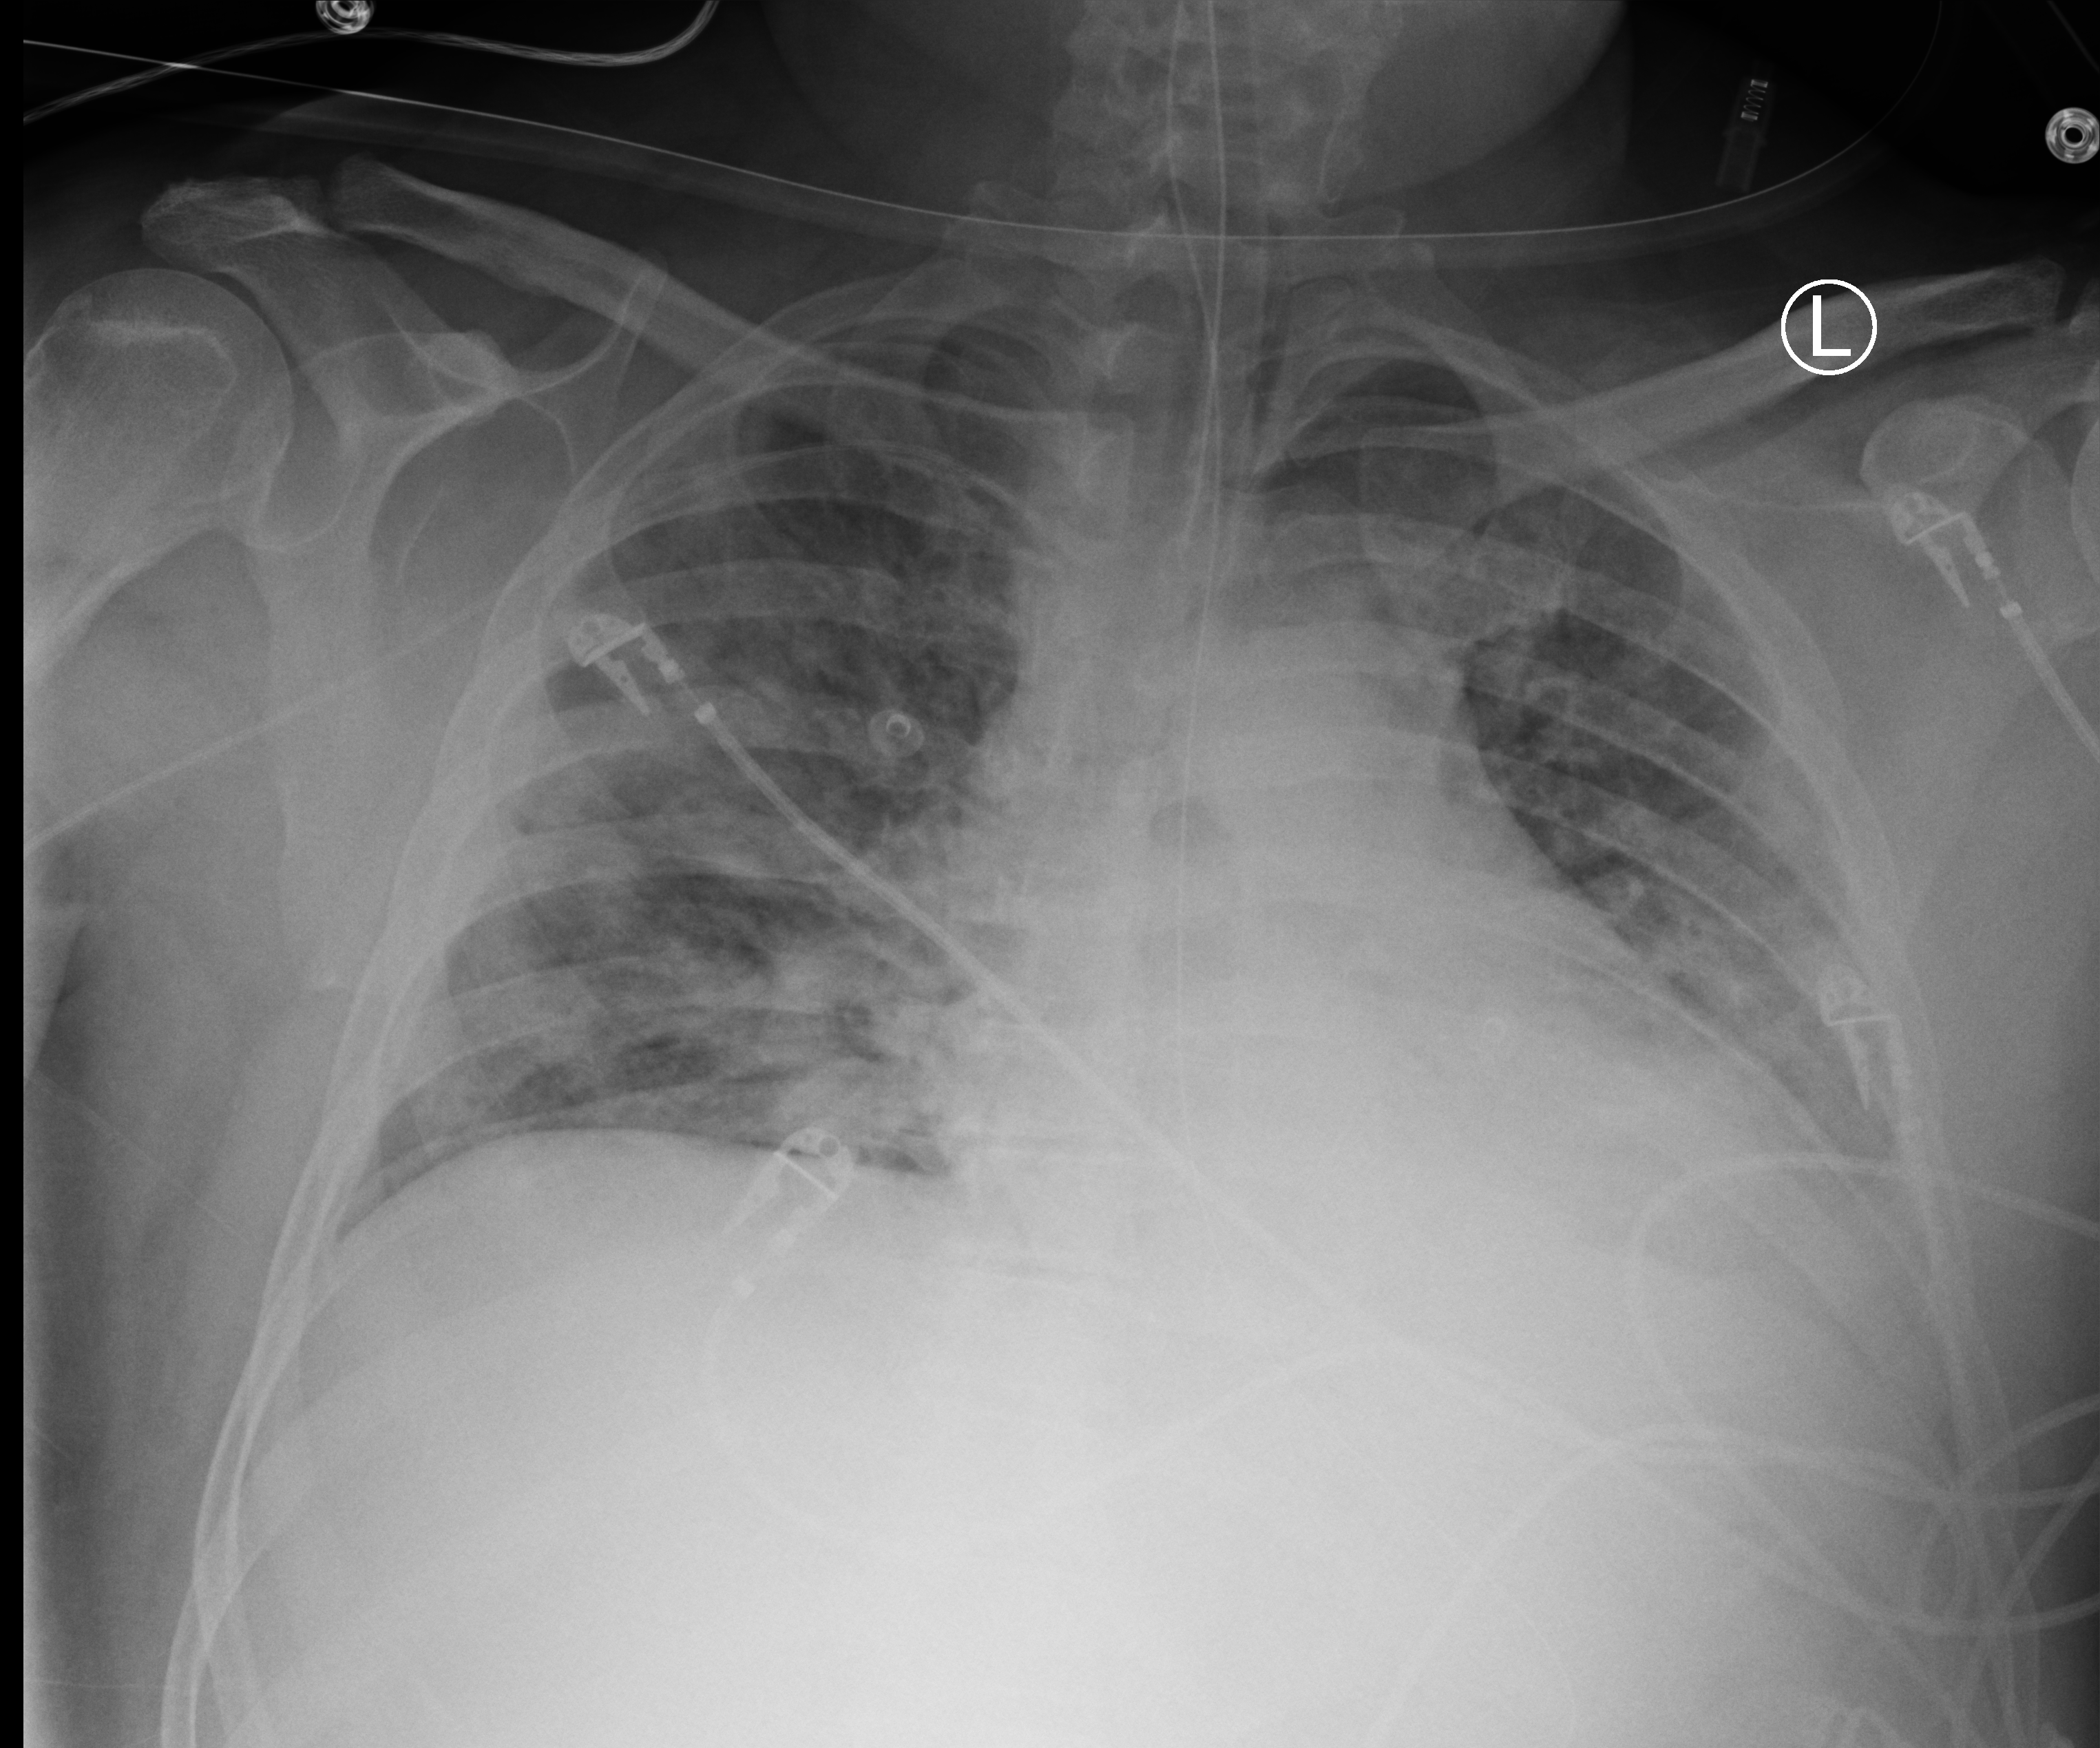
Bedside chest radiograph (computed radiography). Patient hospitalised with COVID-19; male, aged 18–59 years.
Hospital-stay facts (about this admission, not read from this image; timing relative to this image not recorded): mechanically ventilated during this hospital stay: yes; admitted to intensive care during this hospital stay: yes.